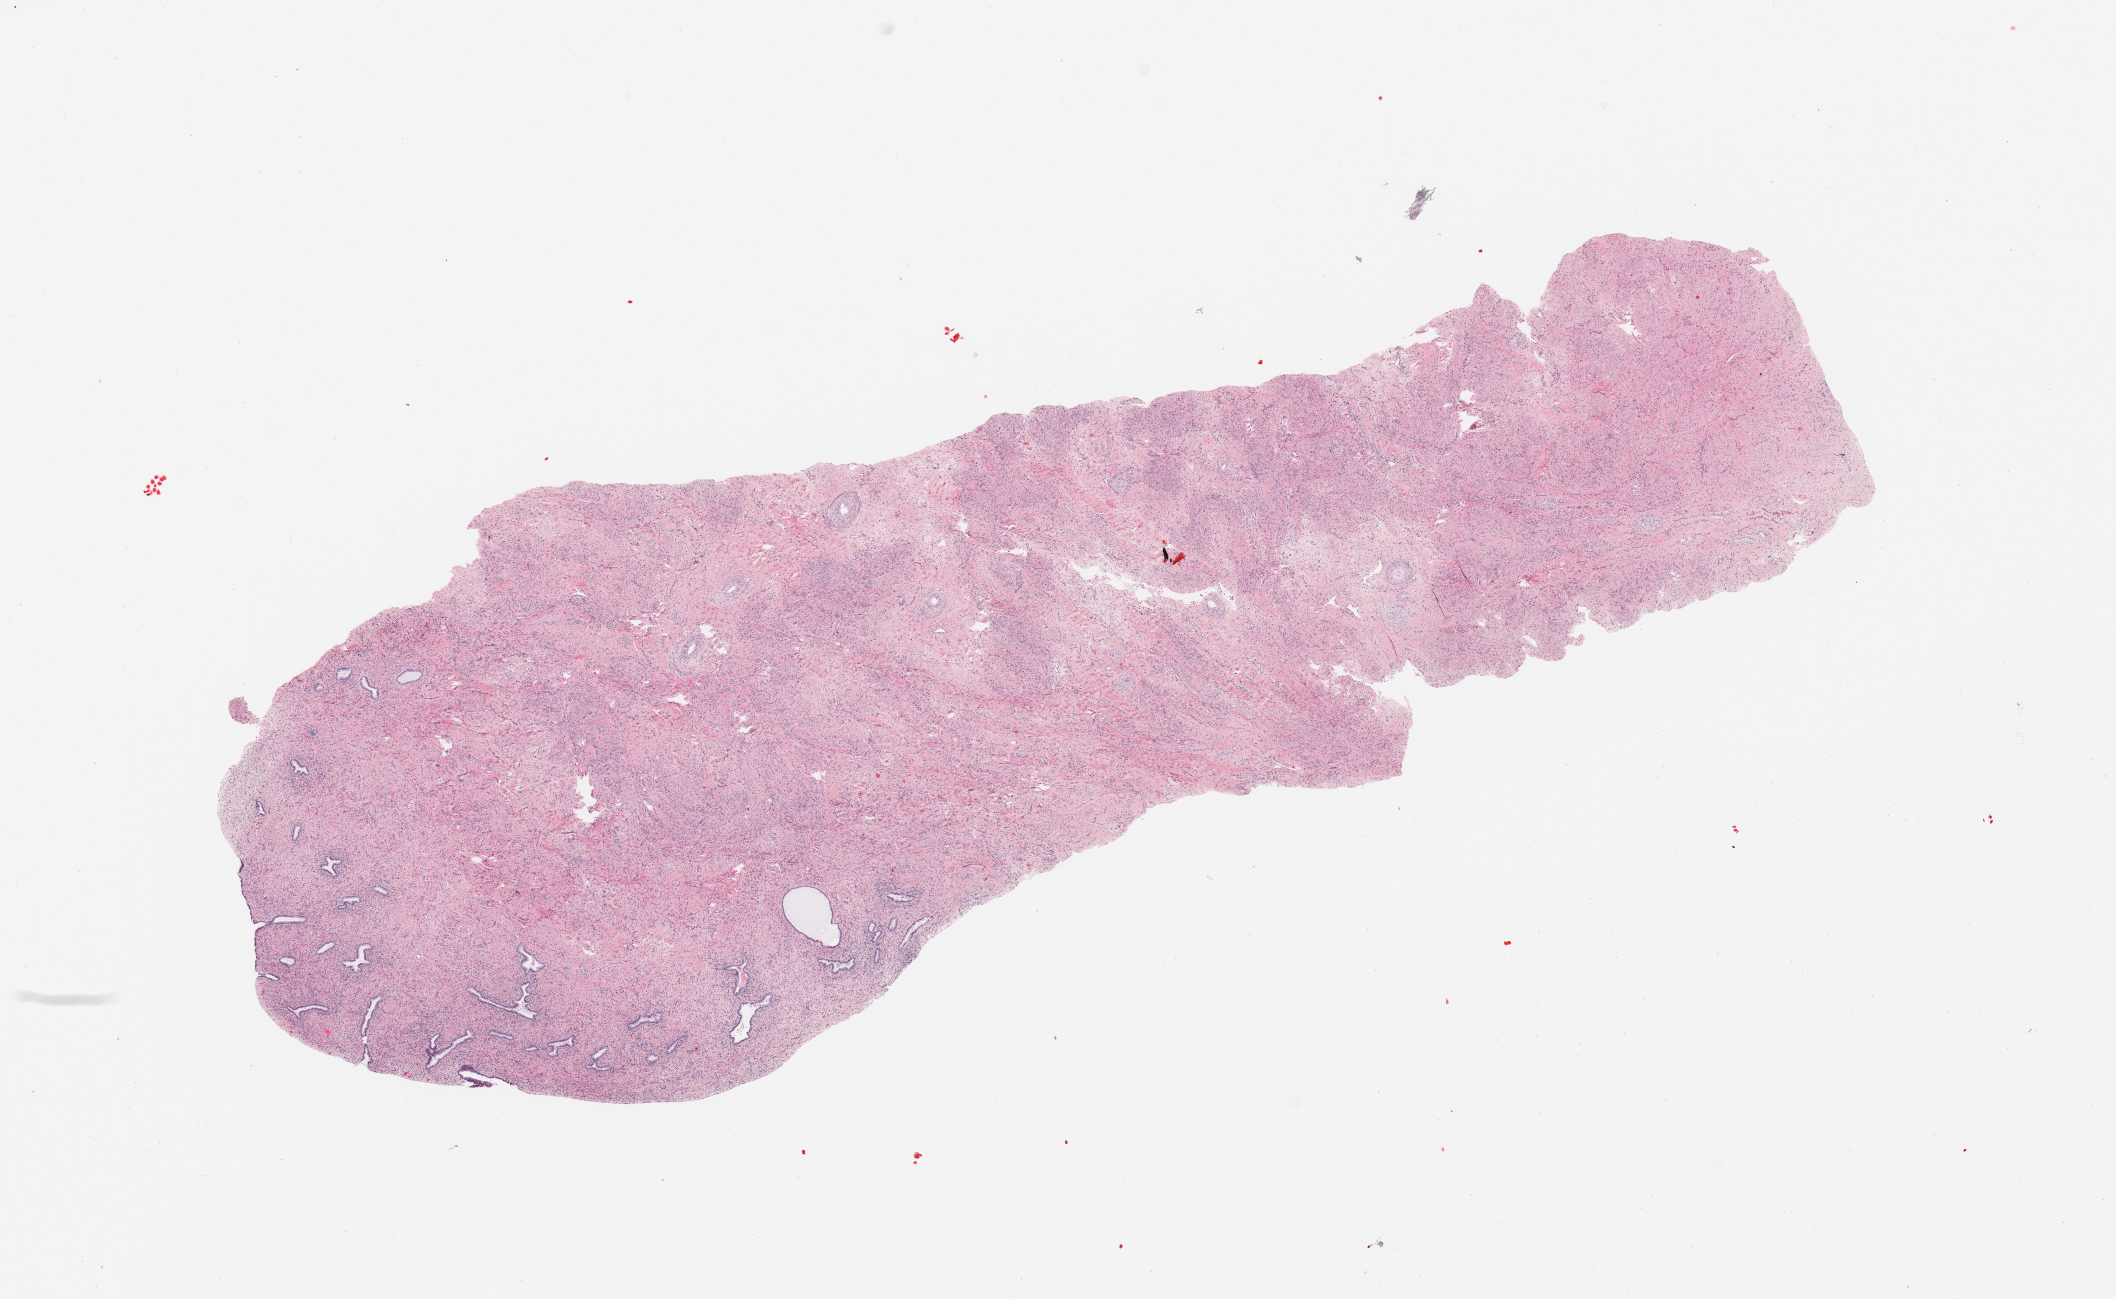
Digitized H&E-stained tissue section (whole slide) — shown as a low-resolution overview of the whole scanned area (about 16.7 x 10.3 mm, from a 20x scan). Normal (non-tumour) tissue sample, uterus. Female, 56 y/o.
This section: normal (non-tumour) tissue from the same patient. Patient diagnosis: Endometrioid adenocarcinoma, NOS.